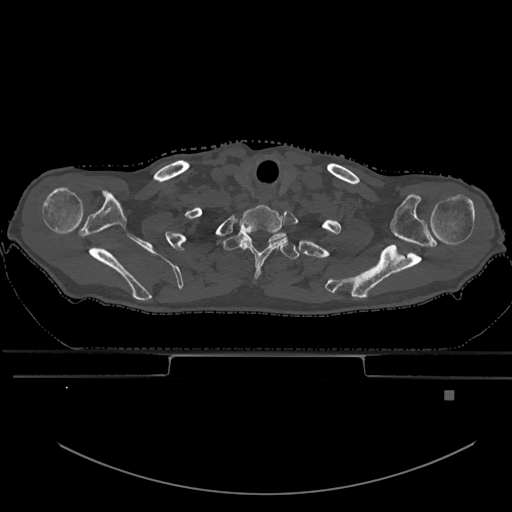
CT including the spine, one axial slice. Slice 555 of 969 in the series (ordered by position). Bone window (W 1800 / L 400 HU). 512 × 512 image matrix, field of view 456 × 456 mm. Male patient, age 82 years. Case-level facts recorded for this patient, not image findings: primary cancer: prostate; vertebrae with lytic lesions (as recorded): T11, T9, T8, T2.
Structures marked on this image (semi-automatically segmented with operator editing):
- T1 vertebra: bounding box <223,232,300,260> (left, top, right, bottom; pixels)